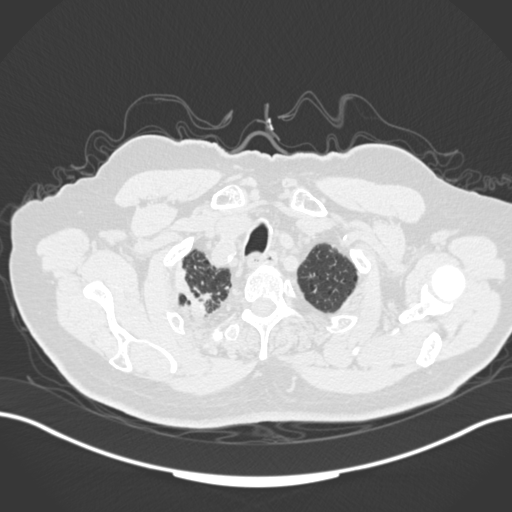
Chest CT, one axial slice. Position 158 of 205 along the scan axis. Lung window (W 1500 / L -600 HU). 1 mm slice thickness. 512 × 512 image matrix, field of view 400 × 400 mm. Patient: male, 72 years. From the clinical record (not read from this slice): clinical TNM (as recorded): T1a N0 M0.
Annotated regions visible in this slice (rectangle marked by the reading radiologist):
- lung tumour (recorded histology: squamous cell carcinoma): bounding box [x1, y1, x2, y2] px = [172, 263, 205, 315]